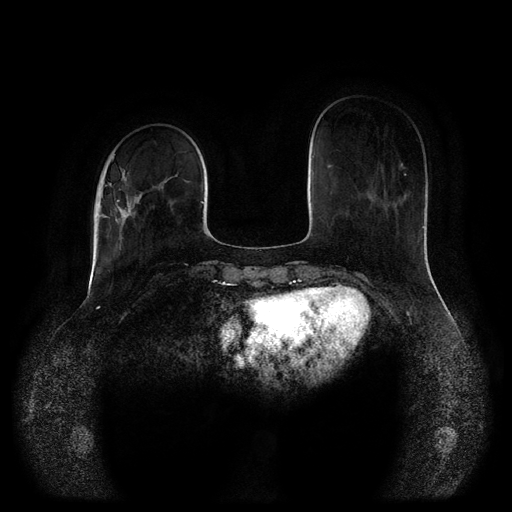
Breast MRI (dynamic contrast-enhanced, multi-phase), one axial slice; position 29 of 116 along the scan axis; dynamic contrast-enhanced series, time point 2 of 5 at this slice position (early post-contrast); 1.5 T; TE 2.6 ms, TR 5.2 ms; 512 × 512 image matrix, field of view 380 × 380 mm. Patient: female, 52 years.
Structures marked on this image (semi-automatically segmented with operator editing):
- breast lesion (labelled 'tumour' in the annotation; benign lesions carry a separate 'benign' label): box from (x=102, y=170) to (x=148, y=253) px